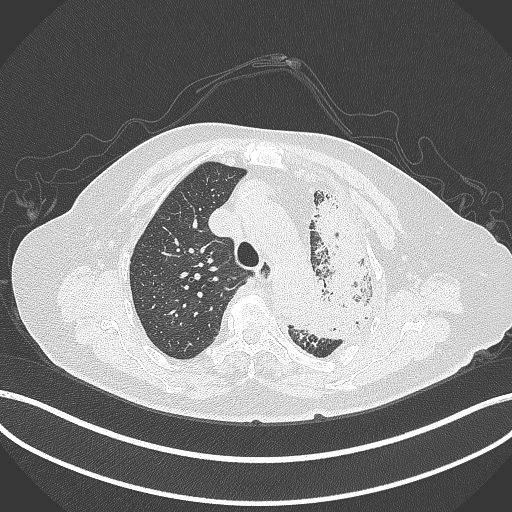
Chest CT, one axial slice; position 295 of 399 along the scan axis; 120 kVp; lung window (W 1500 / L -600 HU); 512 × 512 image matrix, field of view 400 × 400 mm. Female patient, age 75 years. From the clinical record (not read from this slice): clinical TNM (as recorded): T3 N3 M1.
Structures marked on this image (rectangle marked by the reading radiologist):
- lung tumour (recorded histology: adenocarcinoma): bounding box [x1, y1, x2, y2] px = [294, 178, 376, 337]